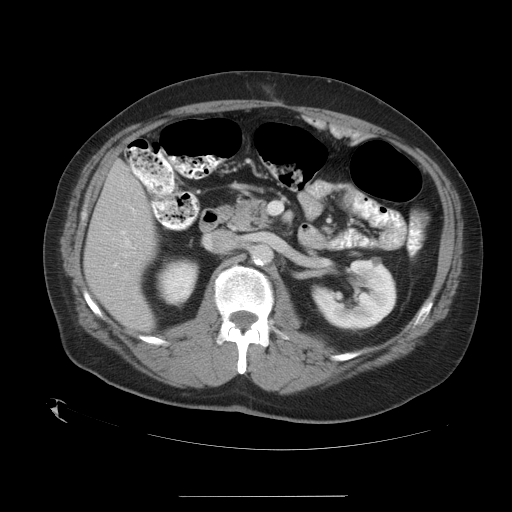
Contrast-enhanced abdominal CT, one axial slice; reconstruction kernel STANDARD; 120 kVp; intravenous contrast given; soft-tissue window (W 400 / L 40 HU); 512 × 512 image matrix. Male patient, age 67 years. Case-level facts recorded for this patient, not image findings: diagnosis: colorectal cancer liver metastases, imaged before liver resection; multiple liver metastases: no; largest metastasis: 2.3 cm; disease in both lobes: no.
Annotated regions visible in this slice (expert manual segmentation):
- liver: bounding box <85,164,156,329> (left, top, right, bottom; pixels)
- planned liver remnant (the part of the liver to remain after resection): <85,165,156,329>
- portal vein (with intrahepatic branches): <121,231,137,253>